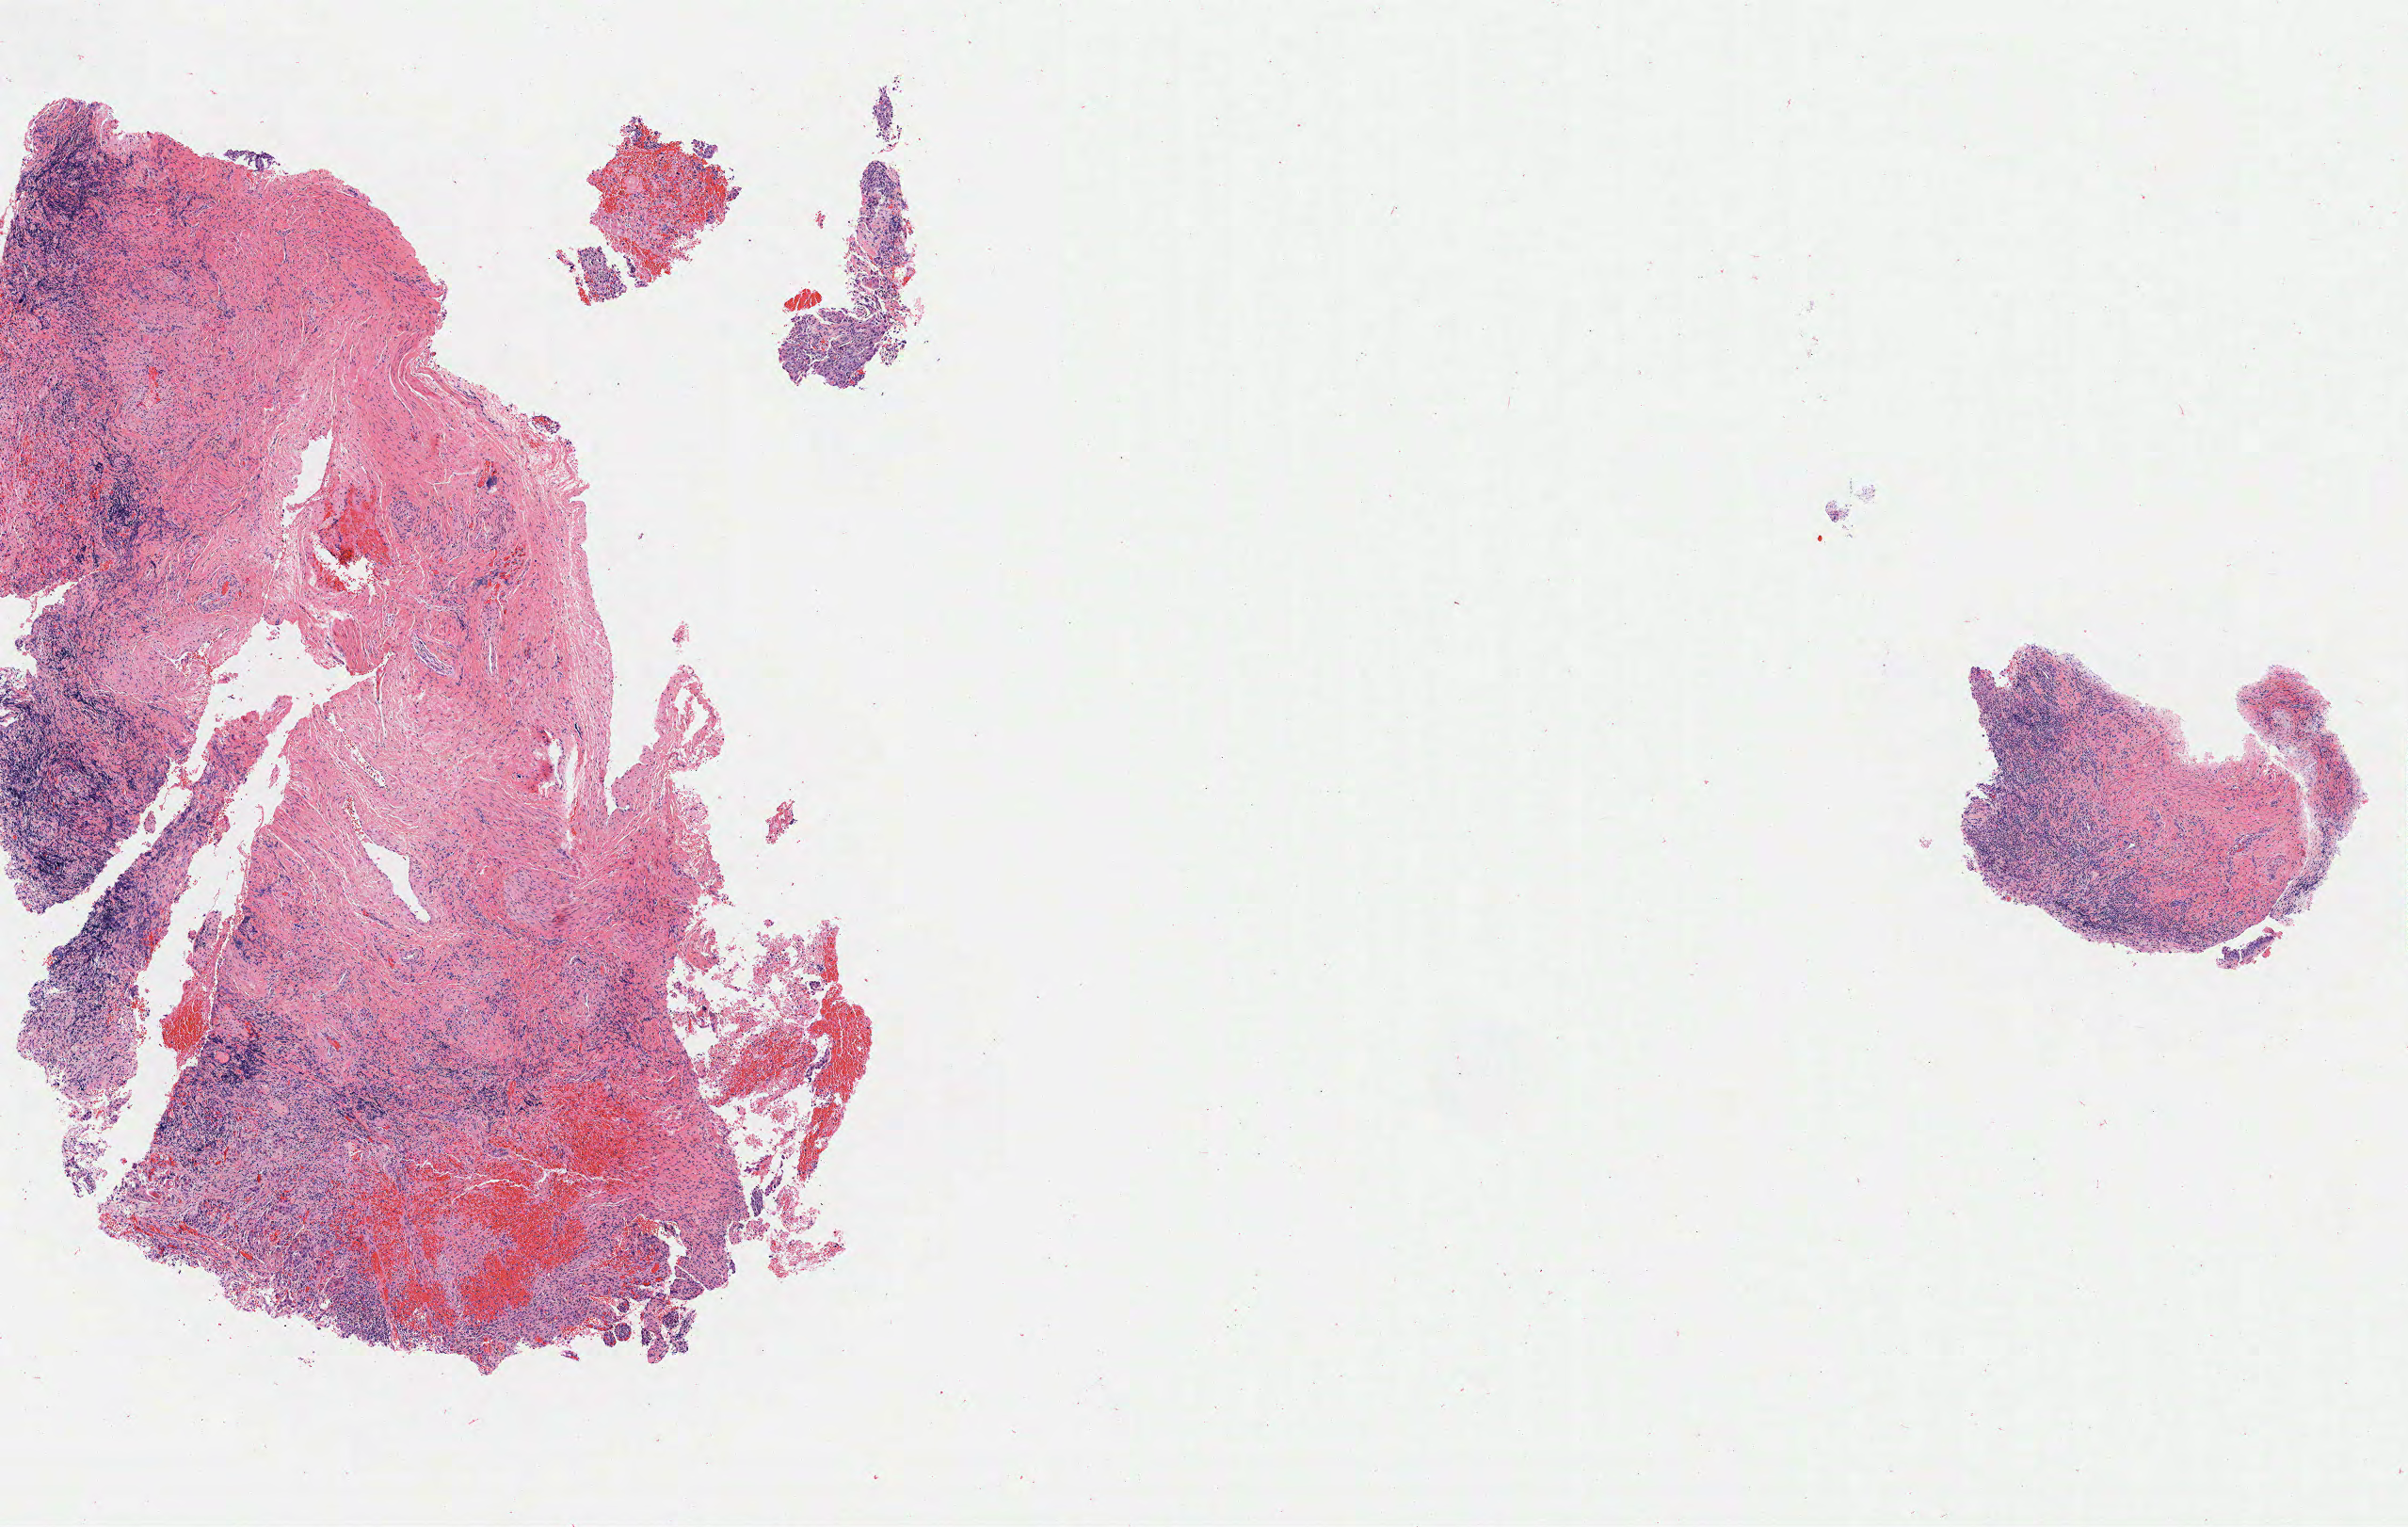
Digitized H&E-stained section, a low-resolution overview of the entire scanned area, about 10.2 x 6.5 mm; specimen: tumor tissue; anatomic site: cervix. Female patient, age 39 years.
Histologic diagnosis: Squamous cell carcinoma, keratinizing, NOS.